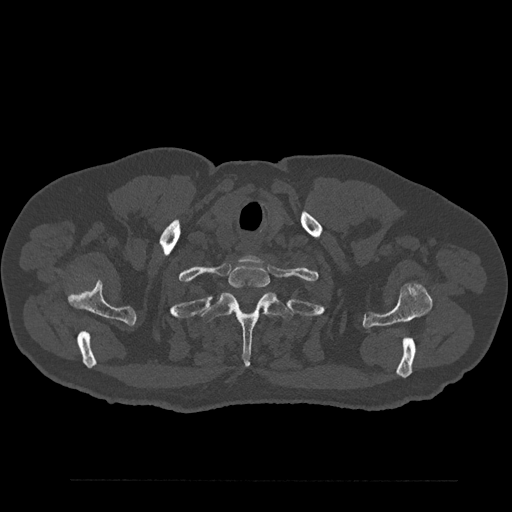
CT including the spine, one axial slice; slice 733 of 797 in the series (ordered by position); 120 kVp; bone window (W 1800 / L 400 HU); 0.5 mm slice thickness; 512 × 512 image matrix. Patient: male, 61 years. Case-level facts recorded for this patient, not image findings: primary cancer: prostate.
Structures marked on this image (semi-automatic segmentation, software-assisted and operator-edited):
- T1 vertebra: bounding box (x1, y1, x2, y2) in pixels: (228, 263, 270, 288)
- T2 vertebra: (202, 293, 293, 366)